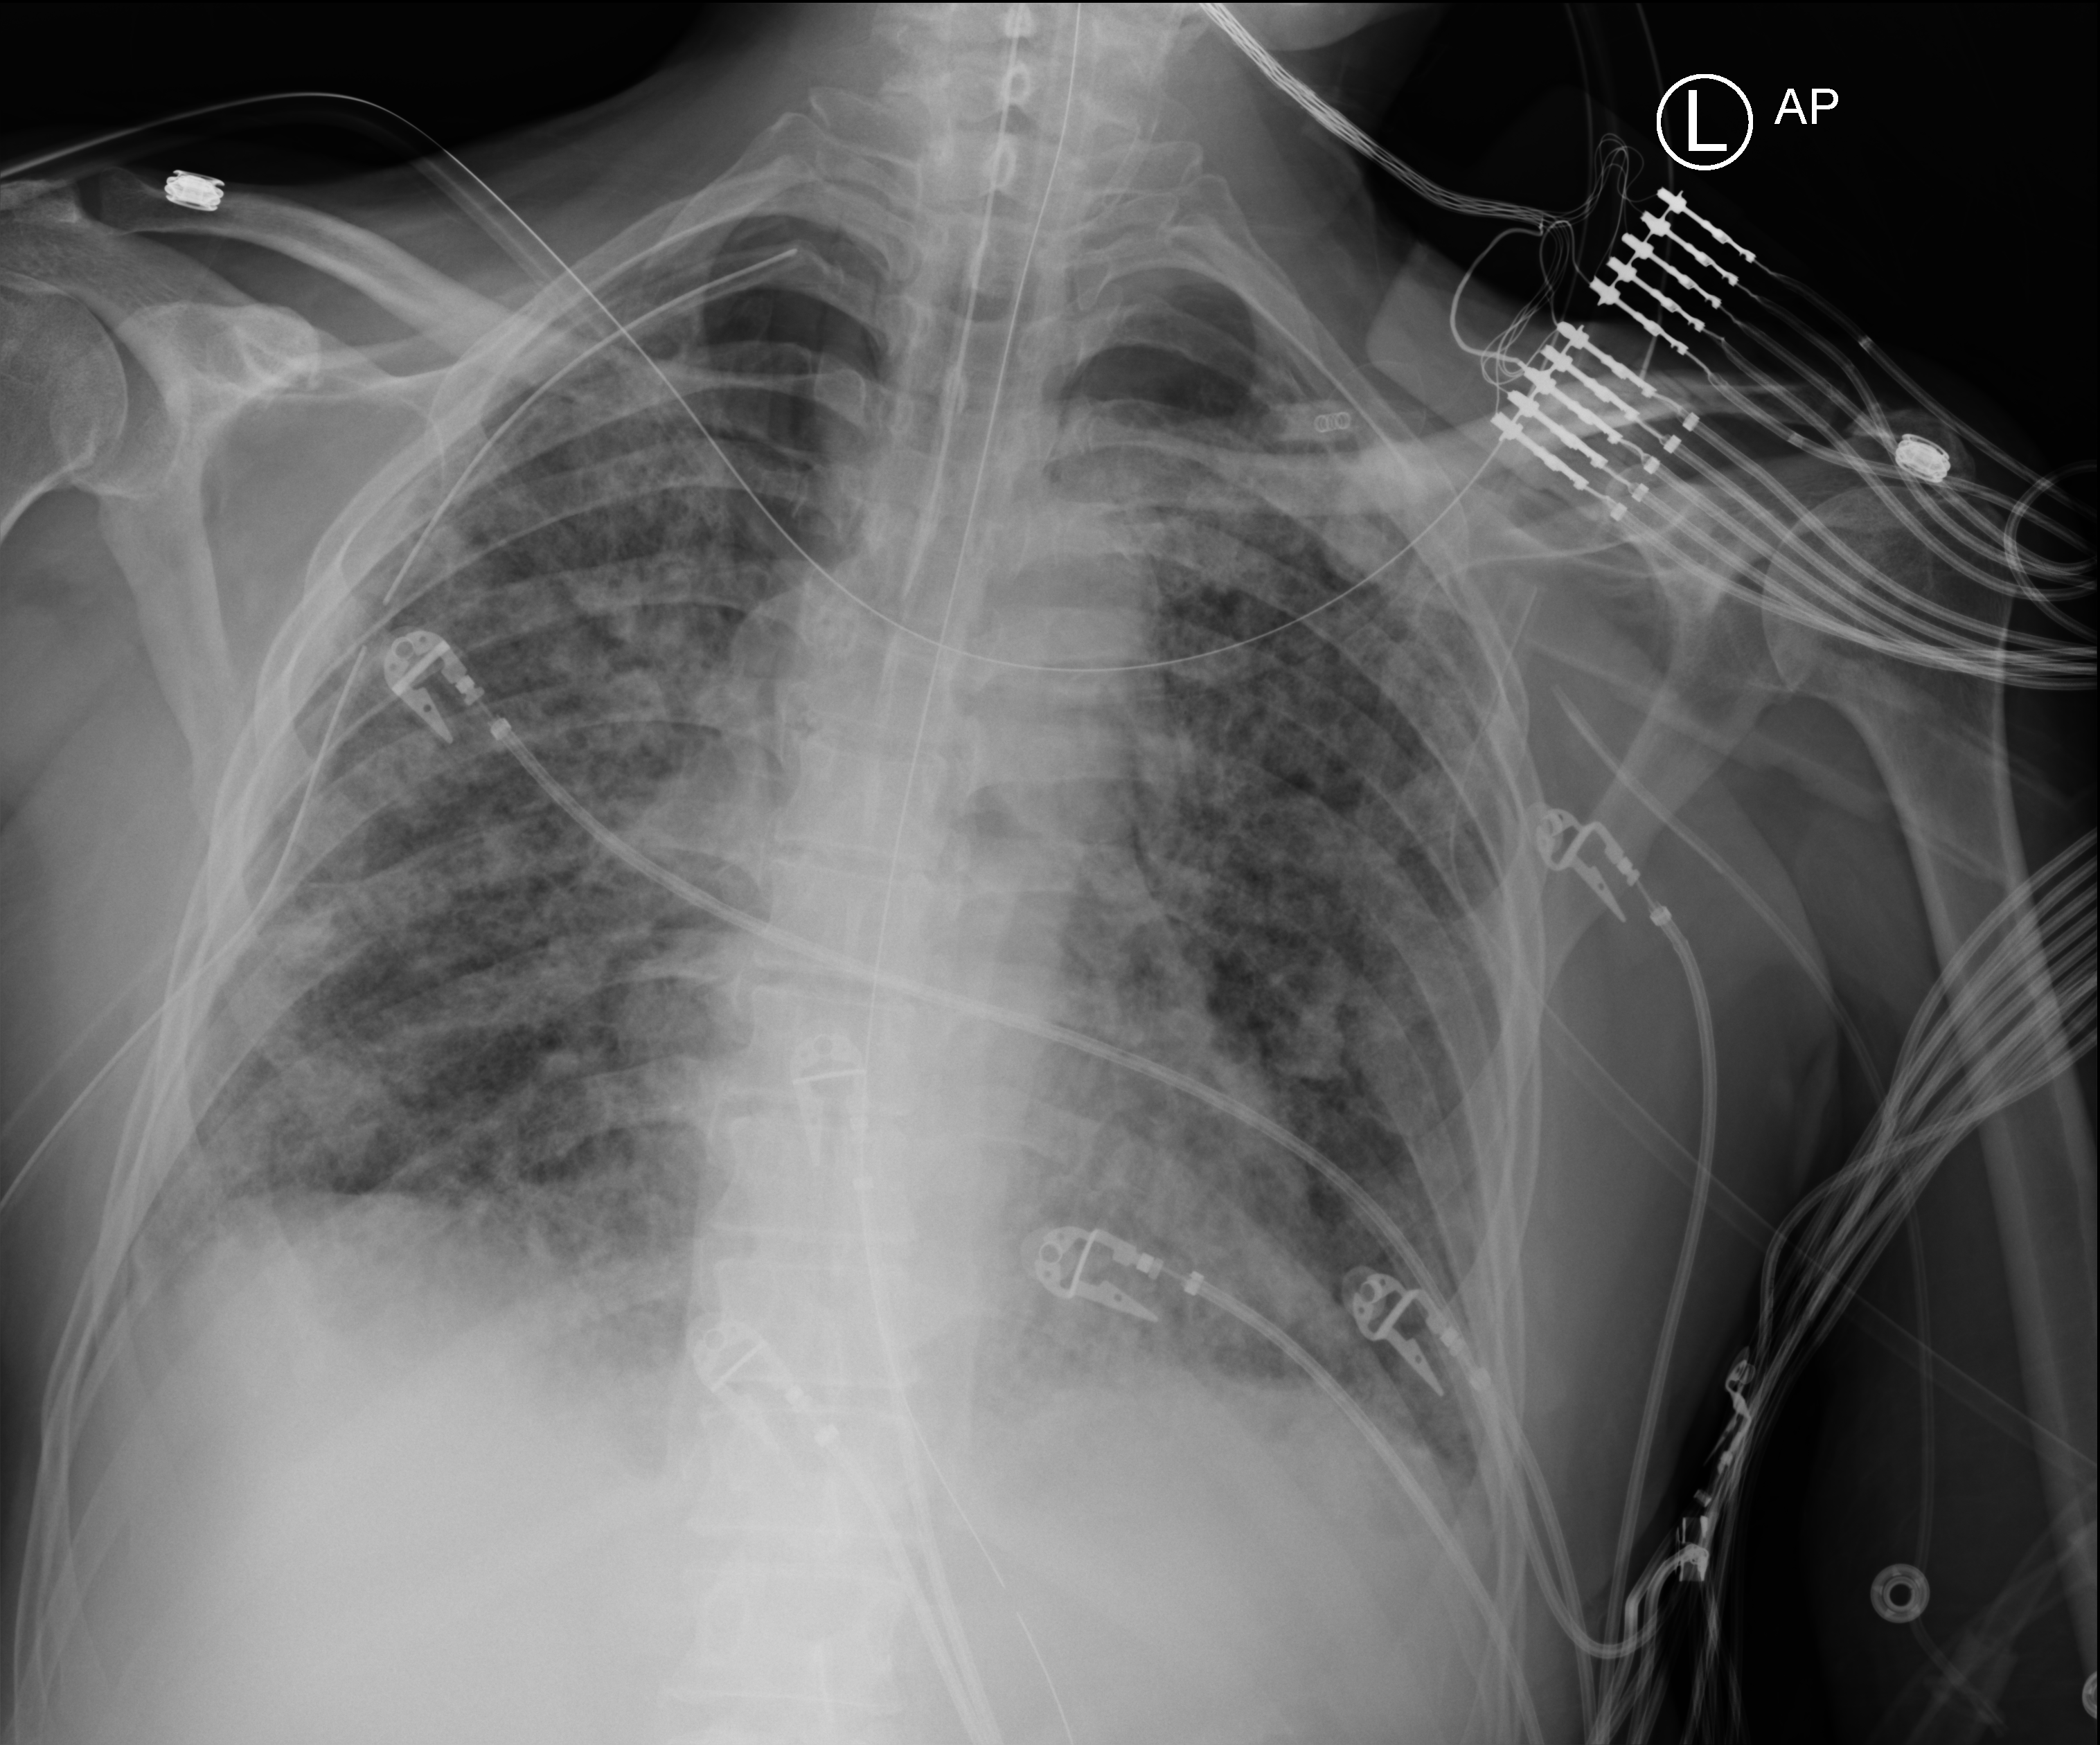
Portable chest radiograph. Male patient hospitalised with COVID-19, age 60–74 years.
Hospital-stay facts (about this admission, not read from this image; timing relative to this image not recorded): other chronic lung disease (admission record): yes.